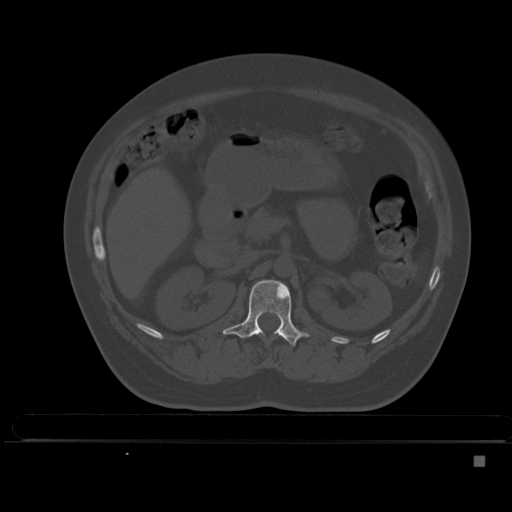
CT including the spine, one axial slice. Bone window (W 1800 / L 400 HU). 1.5 mm slice thickness. 512 × 512 image matrix, field of view 404 × 404 mm. Patient: female, 33 years. Case-level facts recorded for this patient, not image findings: primary cancer: breast; vertebrae with lytic lesions (as recorded): T1.
Outlined on this slice (semi-automatically segmented with operator editing):
- L1 vertebra: box from (x=222, y=280) to (x=309, y=347) px